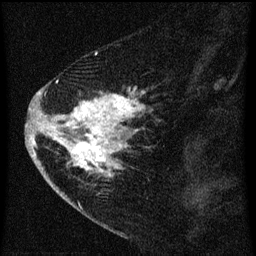
Breast MRI (dynamic contrast-enhanced), one sagittal slice. Position 22 of 60 along the scan axis. Dynamic contrast-enhanced series, image 2 of 3 at this slice position (ordered by acquisition). 1.5 T. TE 4.2 ms, TR 8 ms. 256 × 256 image matrix, field of view 180 × 180 mm. Patient: female, 47 years.
Outlined on this slice (semi-automatically segmented with operator editing):
- analysis volume of interest (the breast-tissue region the enhancement analysis was run in; not a lesion): bounding box (x1, y1, x2, y2) in pixels: (38, 76, 162, 193)
- tumour enhancement mask (voxels above the 70 % enhancement threshold inside the analysis volume of interest): (38, 80, 144, 177)